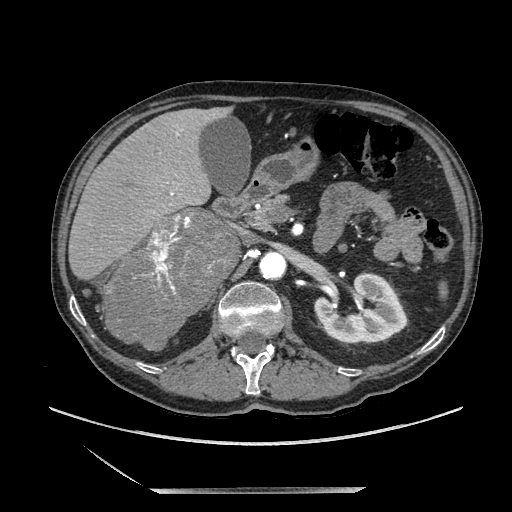
Contrast-enhanced abdominal CT, one axial slice; position 111 of 243 along the scan axis; soft-tissue window (W 400 / L 40 HU); 512 × 512 image matrix, field of view 420 × 420 mm. Male patient. Case-level facts recorded for this patient, not image findings: diagnosis: adrenocortical carcinoma; tumour side: right adrenal; tumour size at pathology: 16 cm; Ki-67 index: 17 %; stage (as recorded): 3.
Outlined on this slice (semi-automatically segmented with operator editing):
- mass: bounding box [x1, y1, x2, y2] px = [106, 210, 239, 348]